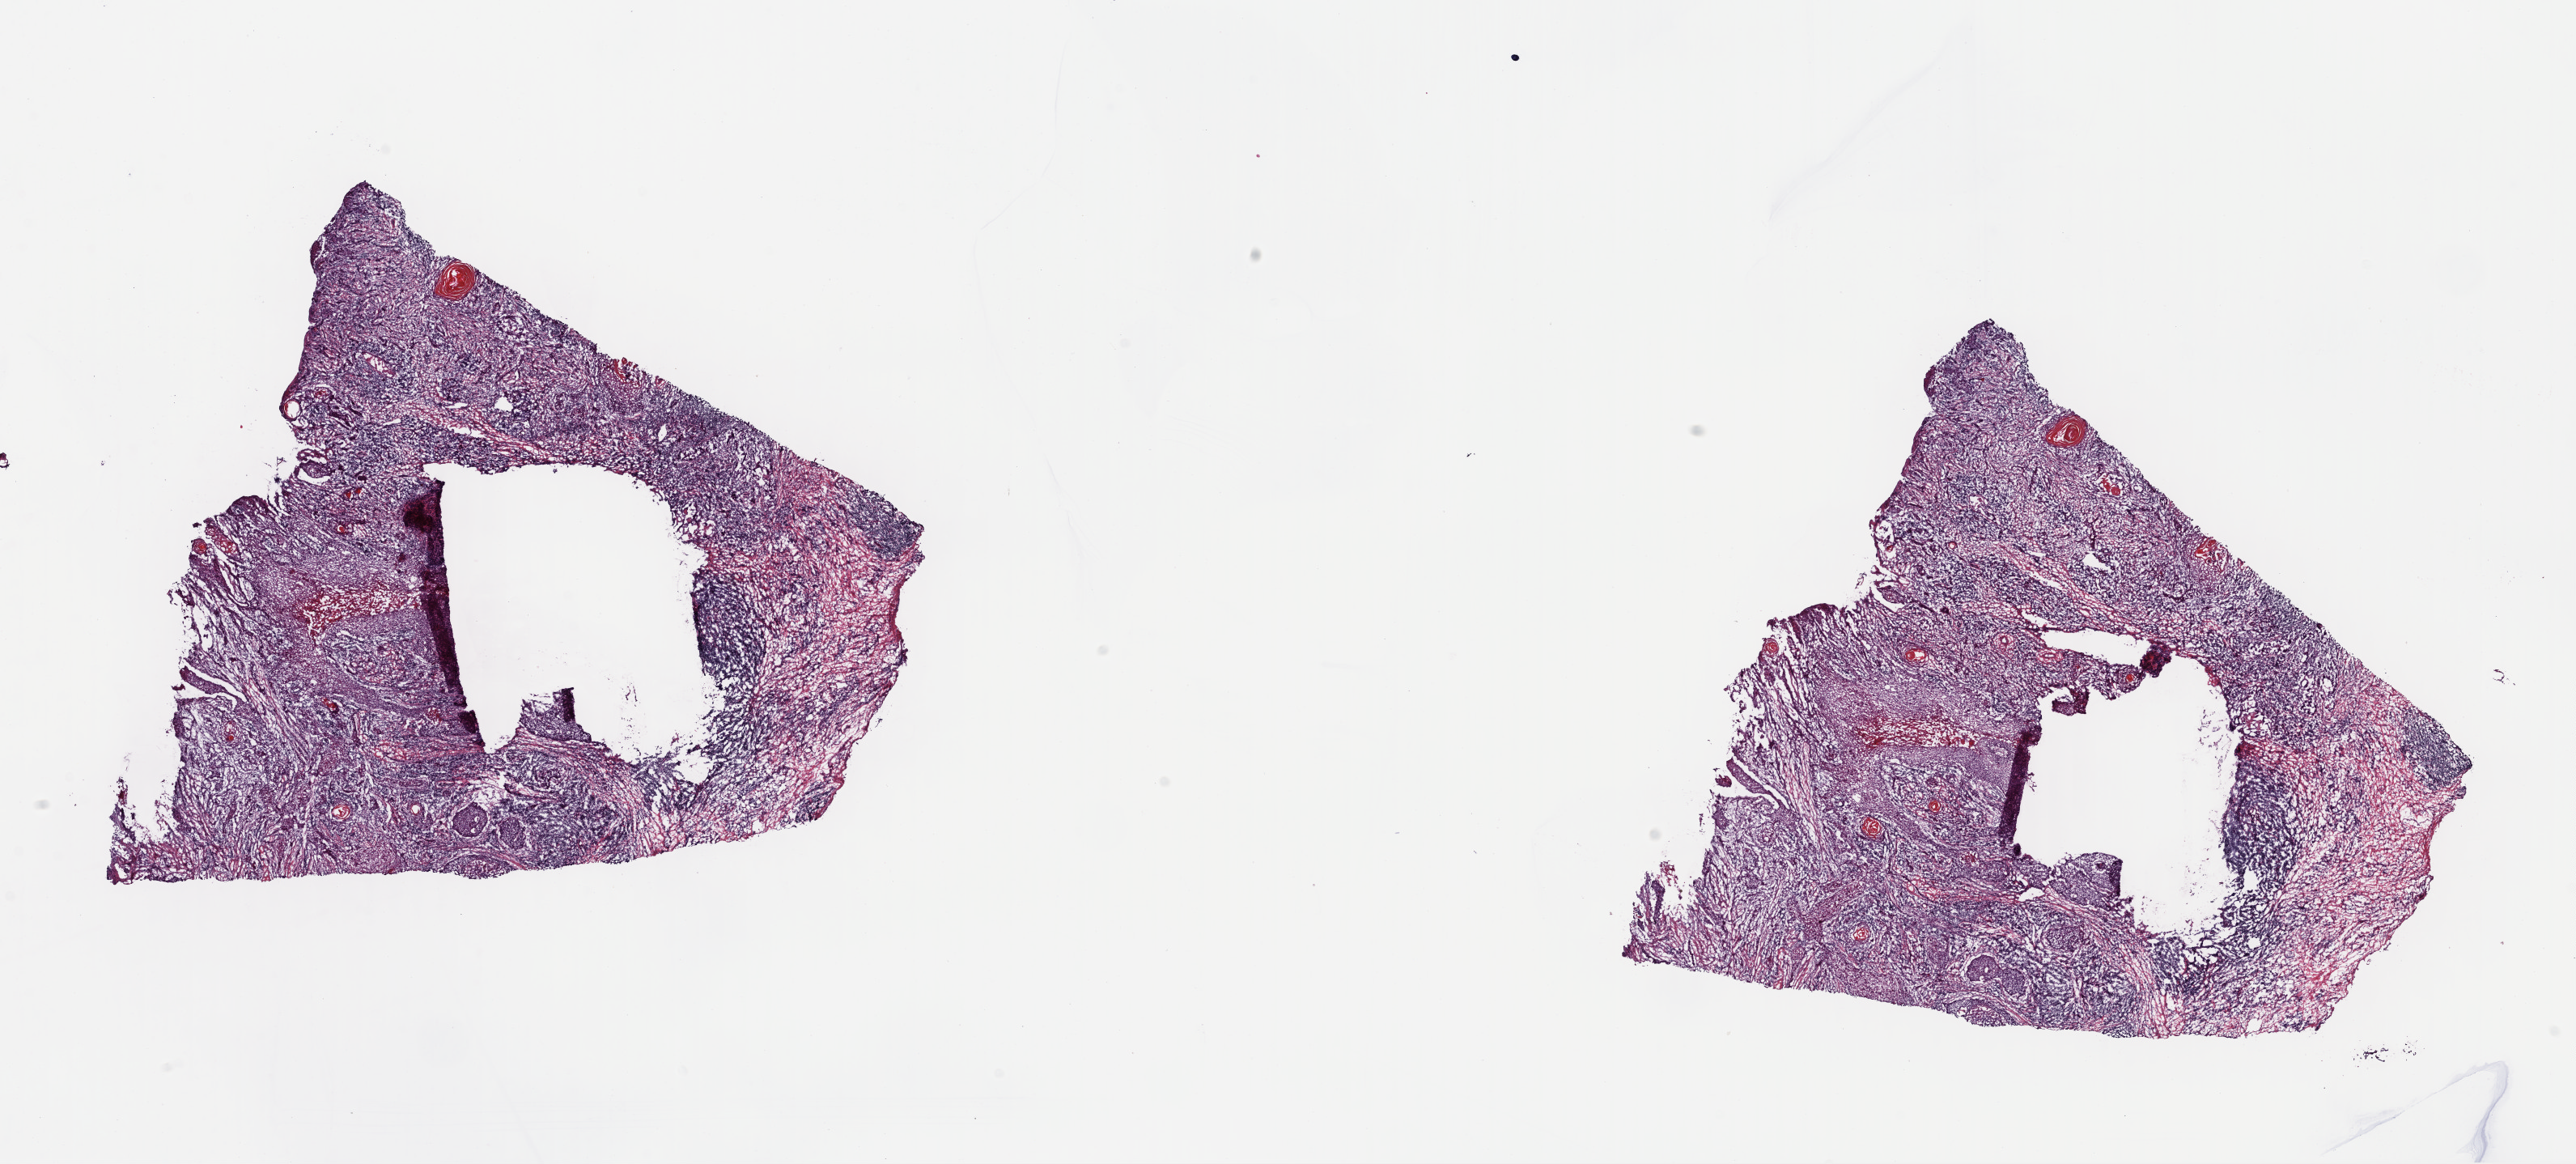
H&E whole-slide image, shown as a low-resolution overview of the whole scanned area (about 25.0 x 11.3 mm); frozen section; sample: primary tumour, head and neck. Male patient; age at initial diagnosis 61 years. Histologic grade: G3 (poorly differentiated). Composition of this section per pathologist review: tumour cells 80%, tumour nuclei 90%, normal cells 0%, stromal cells 15%, necrosis 5%. Inflammatory infiltration, as recorded: lymphocyte infiltration 0%, monocyte infiltration 0%, neutrophil infiltration 0%.
AJCC pathologic stage: IVA (5th edition). Lymph nodes positive (case pathology): 0 of 15 examined. Pathologic diagnosis: Squamous cell carcinoma, NOS (larynx, NOS).